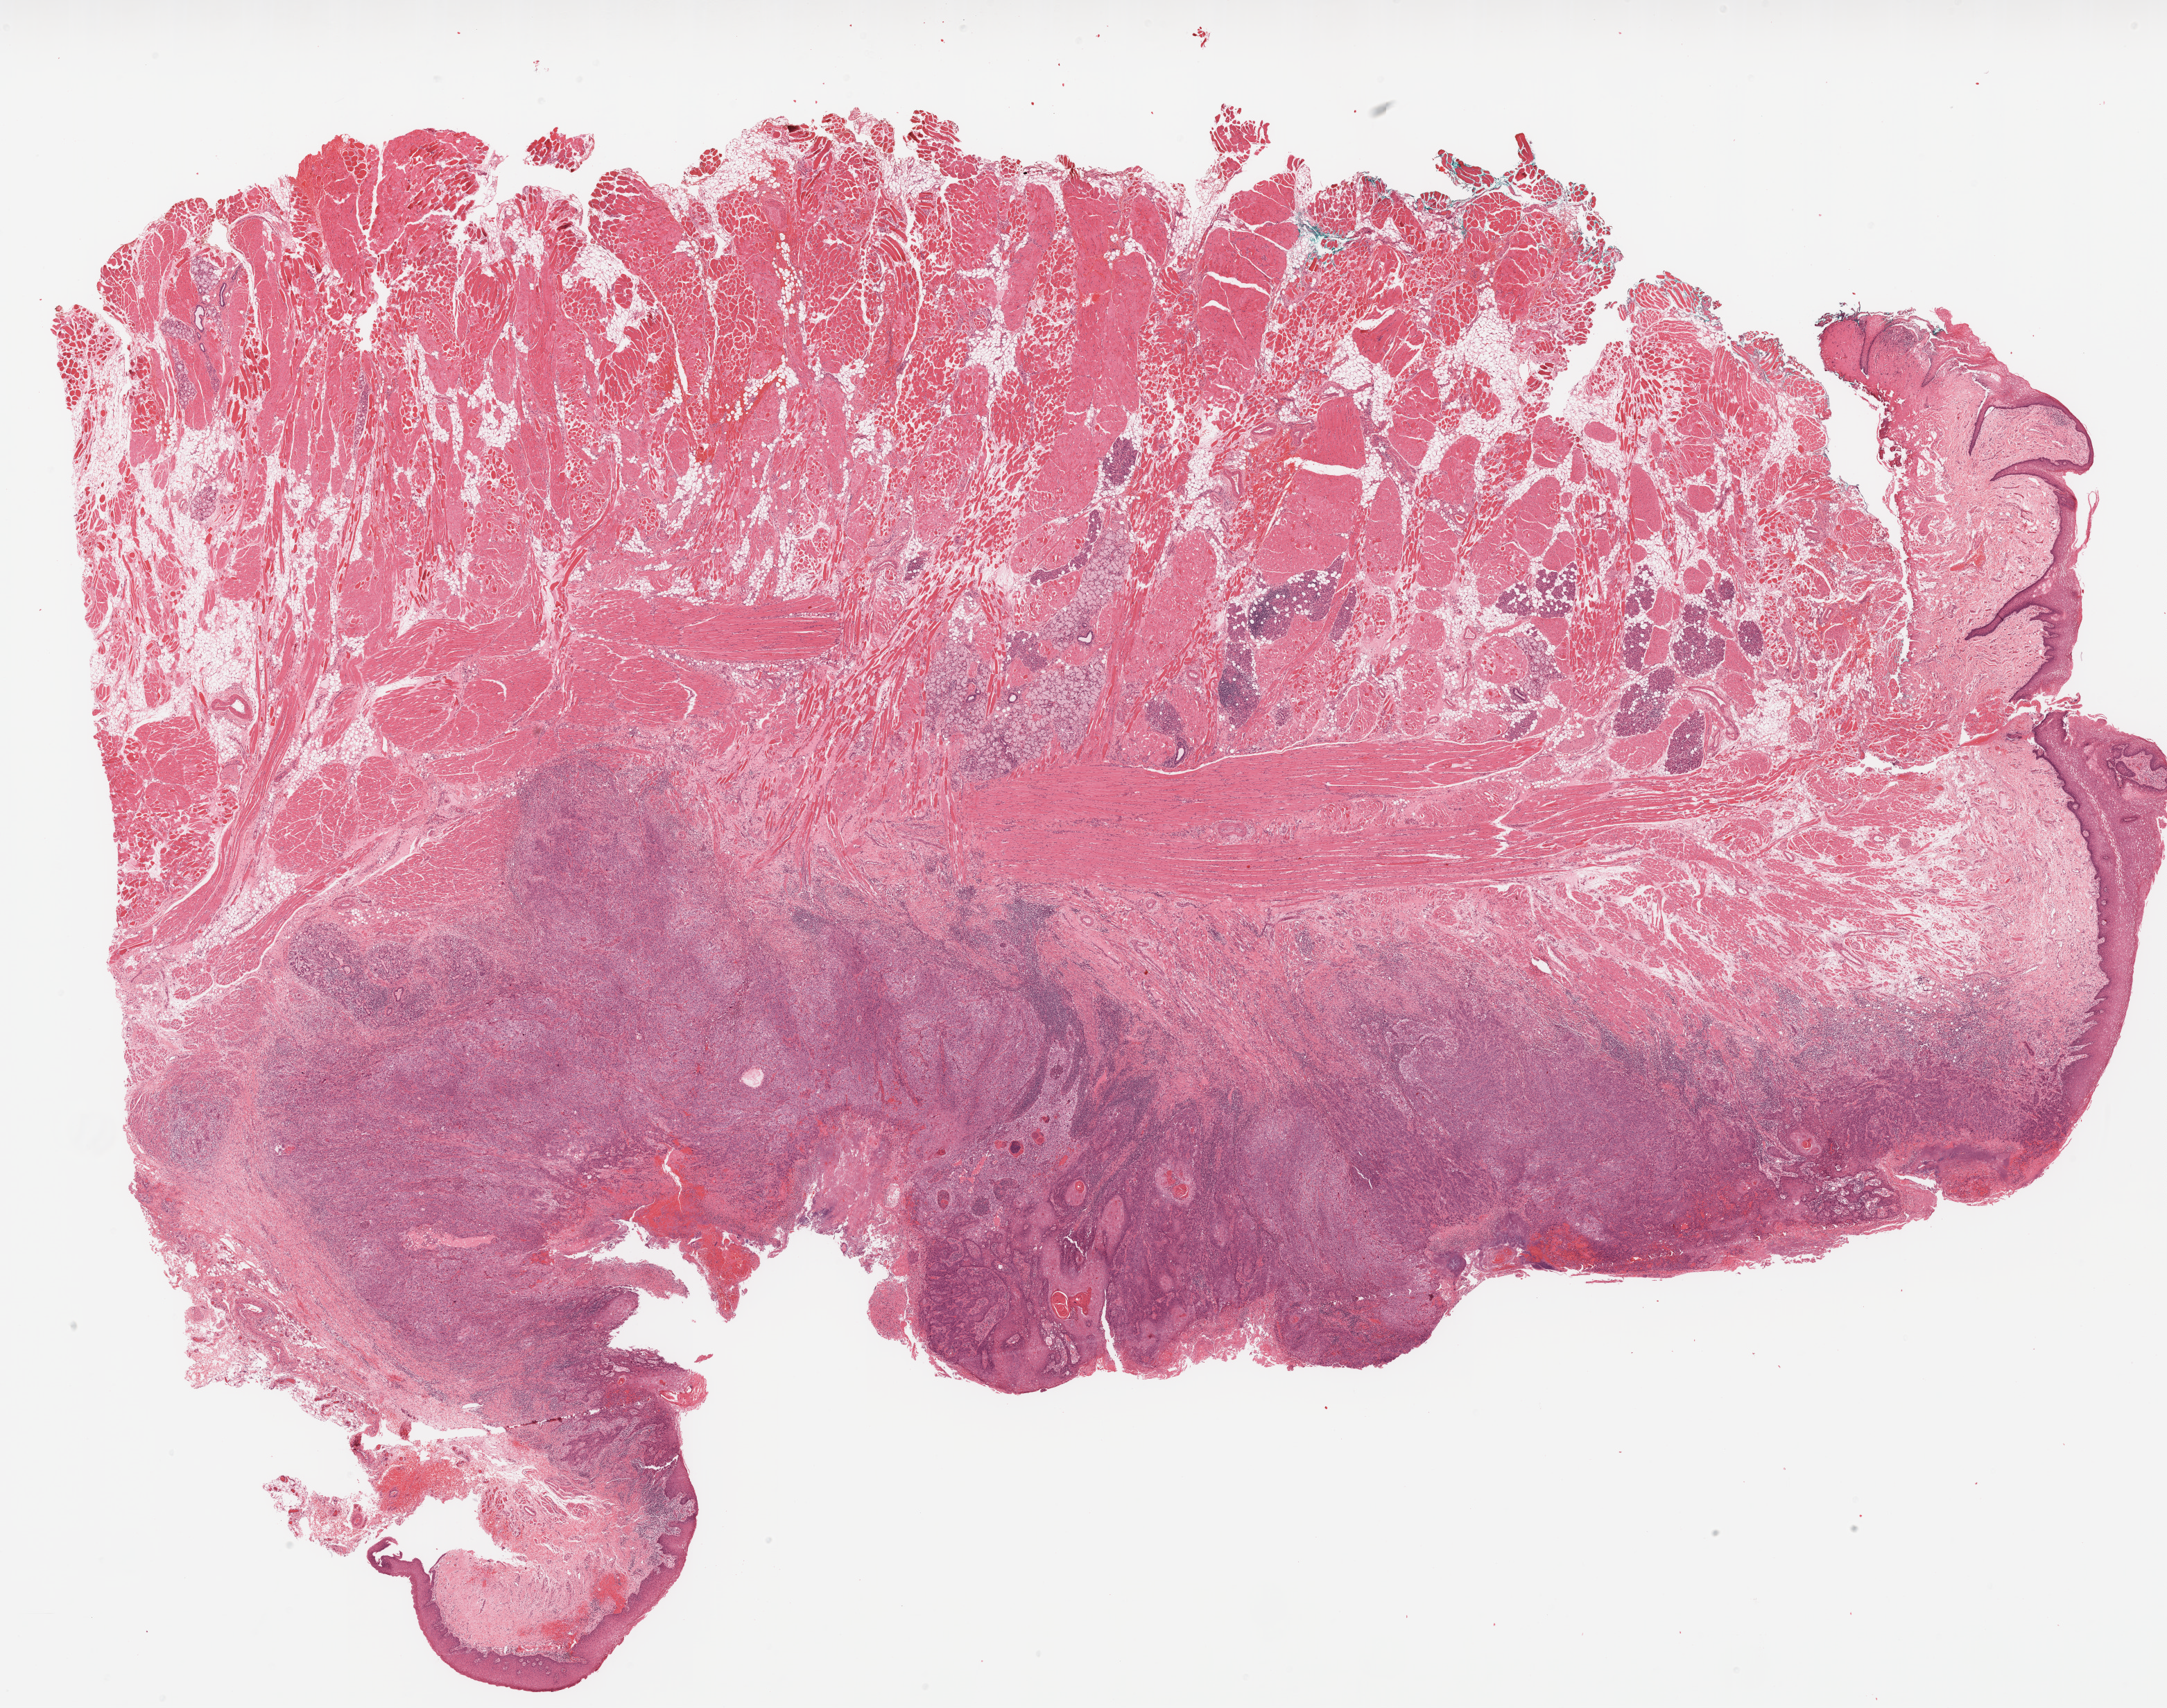
H&E-stained whole-slide image — shown as a low-resolution overview of the whole scanned area (about 25.1 x 19.8 mm, from a 20x scan). FFPE section. Head and neck, primary tumour sample. Female patient; age at initial diagnosis 46 years. Histologic grade: G2 (moderately differentiated).
AJCC pathologic stage: II (6th edition). TNM: T2 N0. Diagnosis: Squamous cell carcinoma, NOS (tongue, NOS).